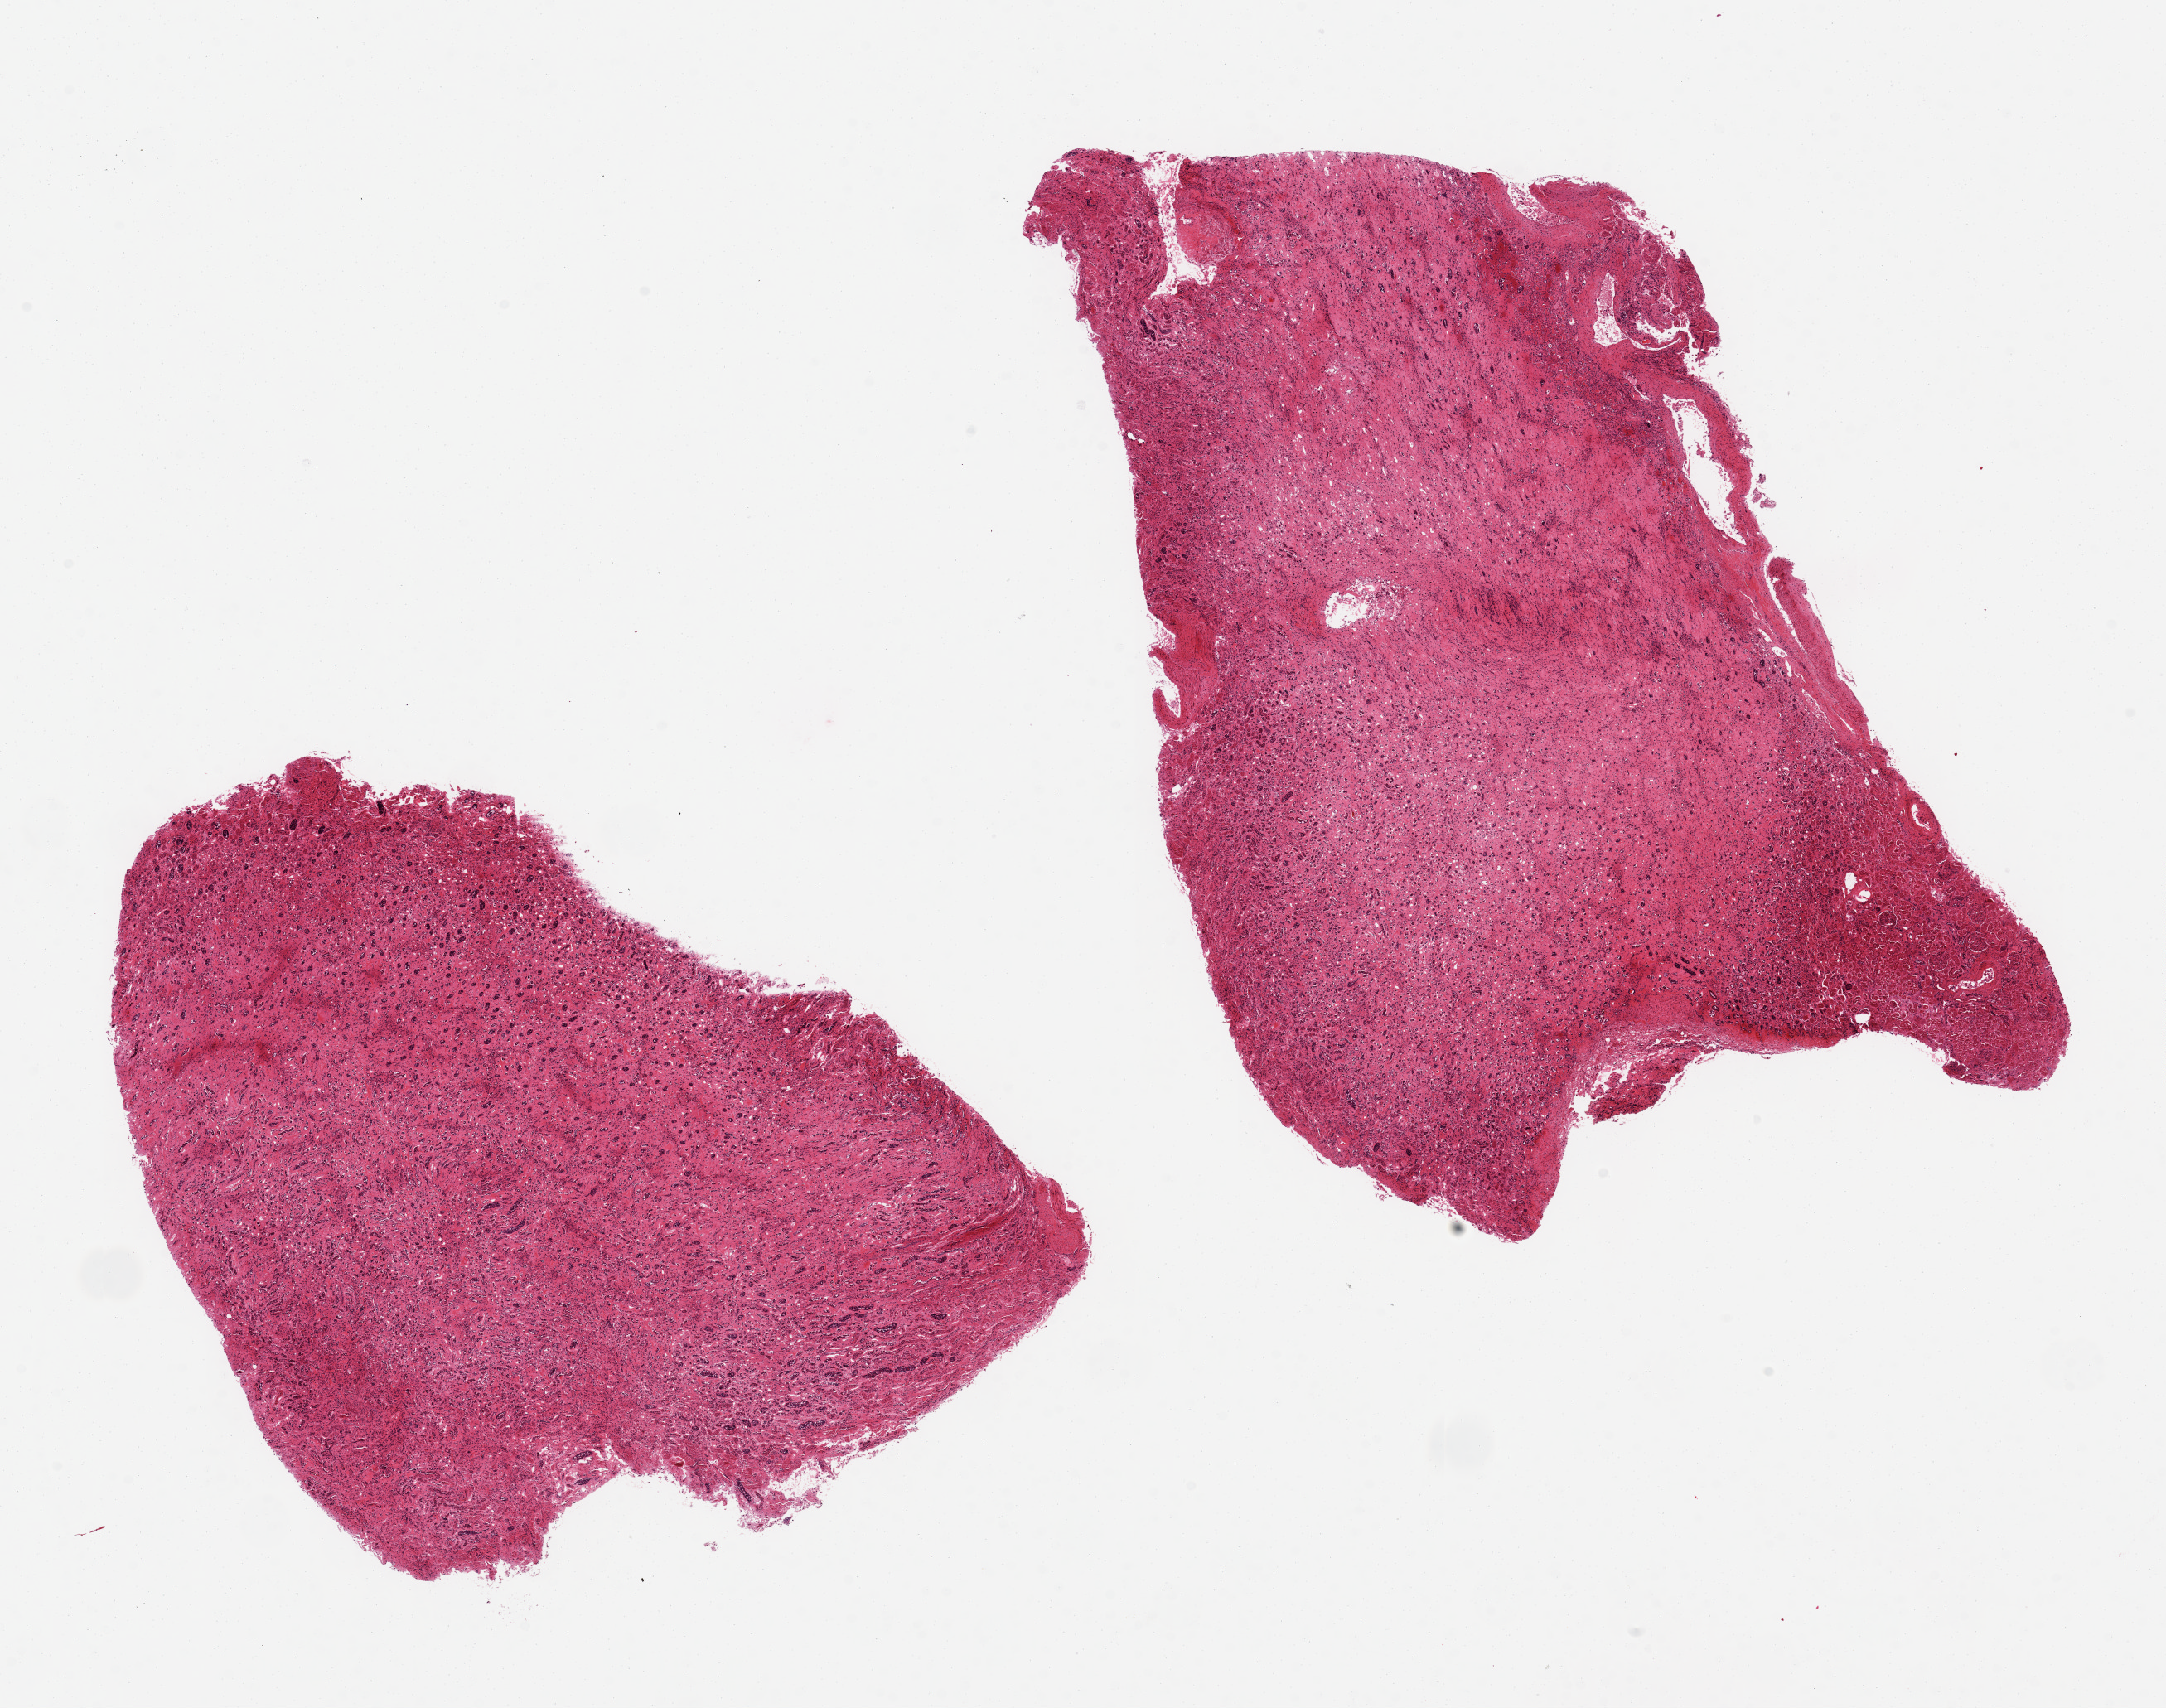
Digitized hematoxylin and eosin (H&E)-stained section, brightfield, whole scanned area (about 20.7 x 16.3 mm) shown as a low-resolution overview; PAXgene-fixed paraffin-embedded (PFPE) section; section of renal medulla (target tissue); tissue donor sample.
Pathologist's review note for this sample: 2 pieces, 10x7 & 8x7 mm; all medulla no cortex.